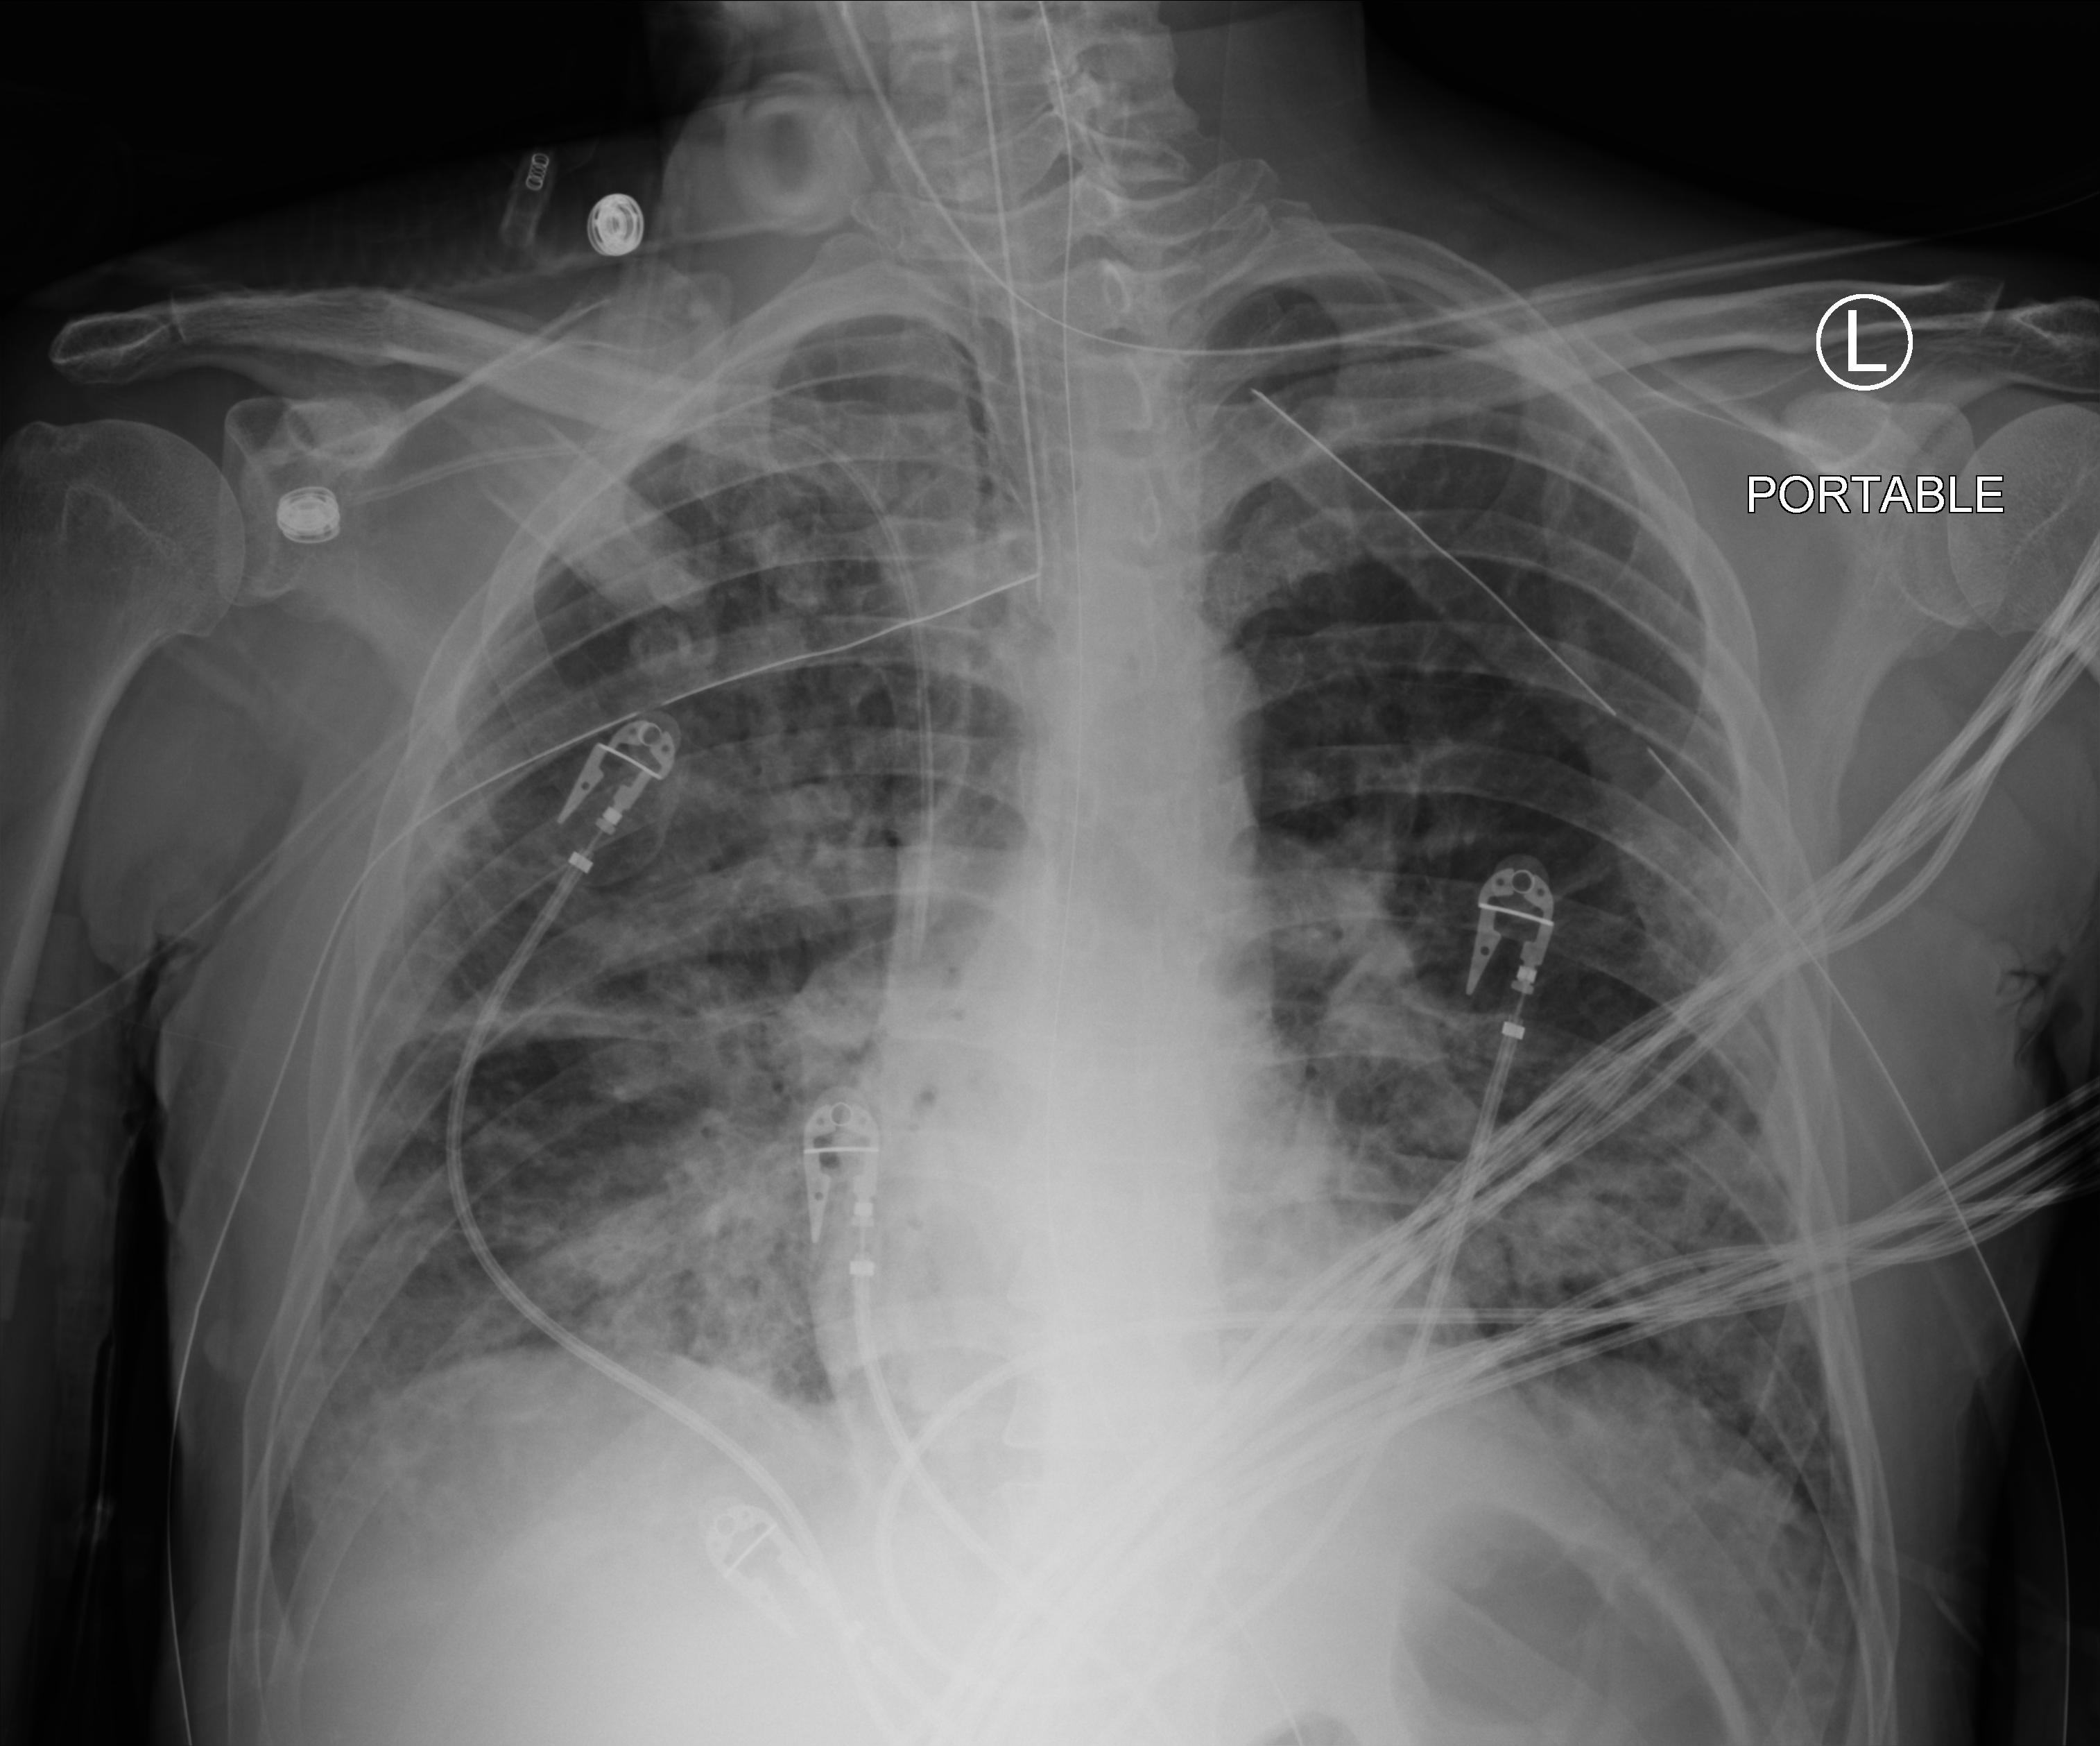
Bedside chest radiograph (computed radiography); anteroposterior (AP) projection. Patient hospitalised with COVID-19; male, aged 18–59 years.
From the hospital-stay record, not from the radiograph (when in the stay this image was taken is not recorded): admitted to intensive care during this hospital stay: yes; COPD (admission record): no; diabetes (admission record): yes.